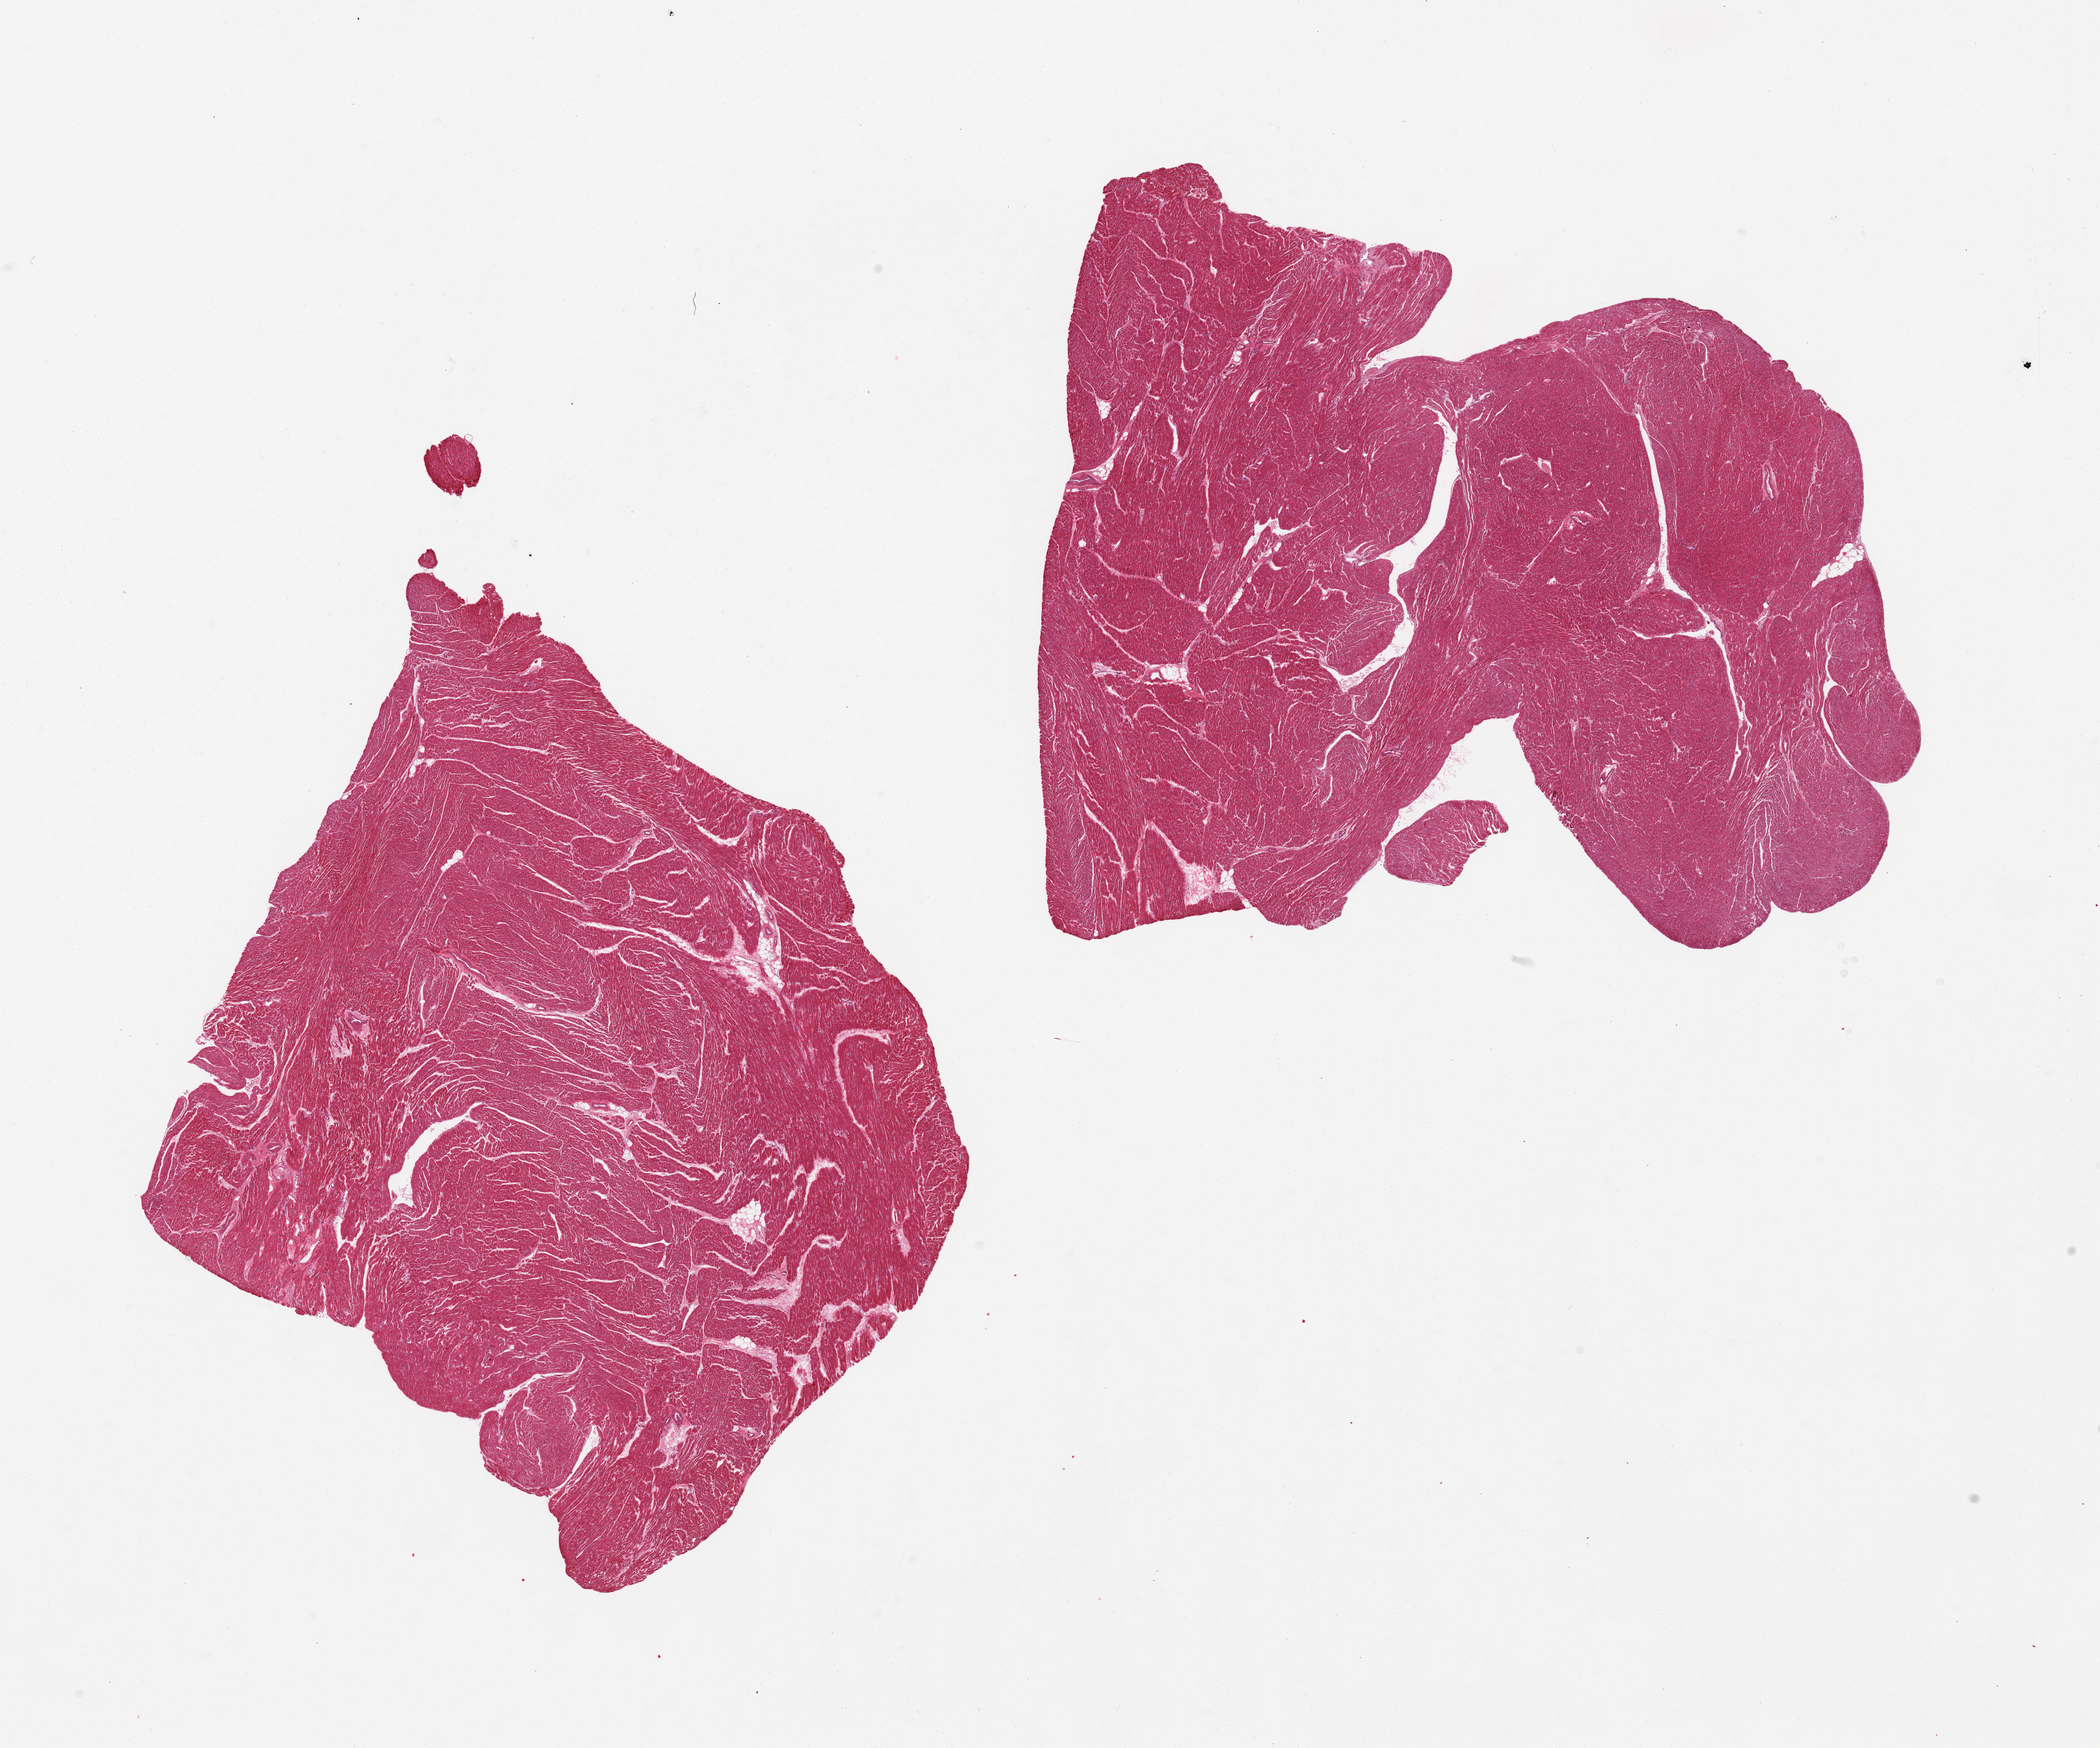
Digitized H&E-stained section, brightfield — a low-resolution overview of the entire scanned area, about 24.6 x 20.5 mm; PAXgene-fixed, paraffin-embedded tissue; sampled site (target tissue): heart; donor tissue sample. Donor: male.
* reviewer comment on this tissue sample: 2 pieces no significant ischemic changes